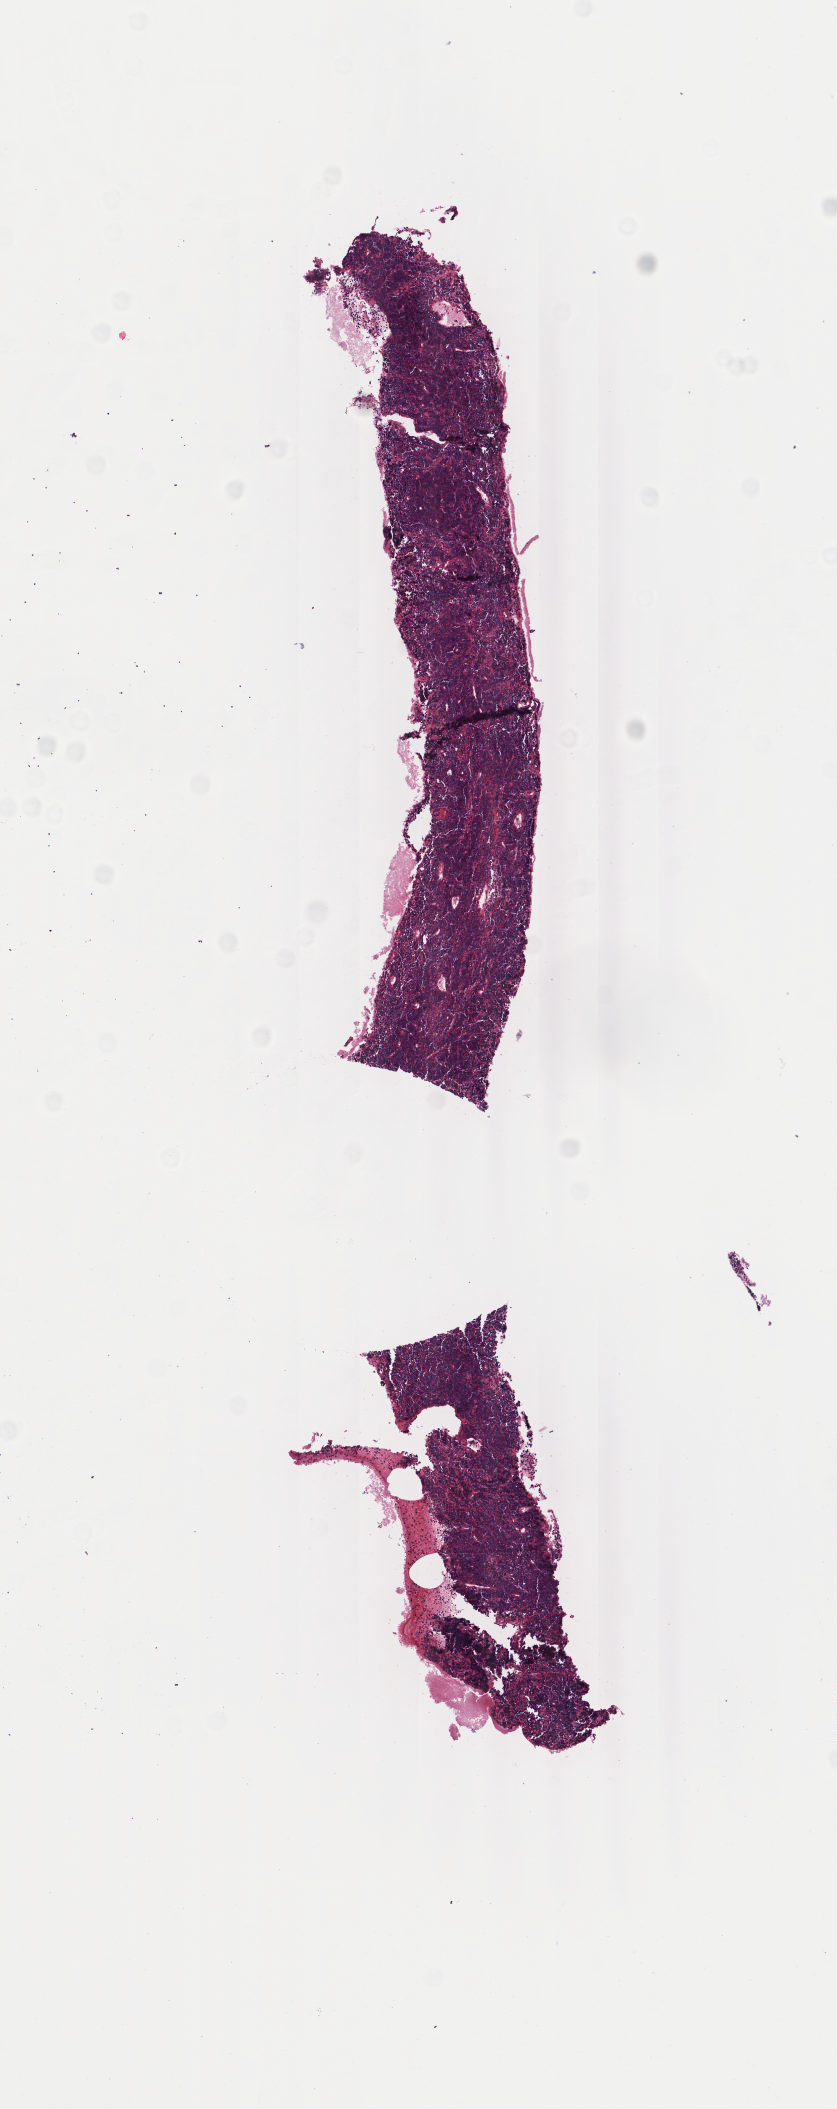
Digitized haematoxylin and eosin-stained section — shown as a low-resolution overview of the whole scanned area (about 3.3 x 8.4 mm). Specimen: tumor tissue. Site: abdominal lymph node. Female patient; age at initial diagnosis 6 years.
Histologic diagnosis: Burkitt lymphoma, NOS.